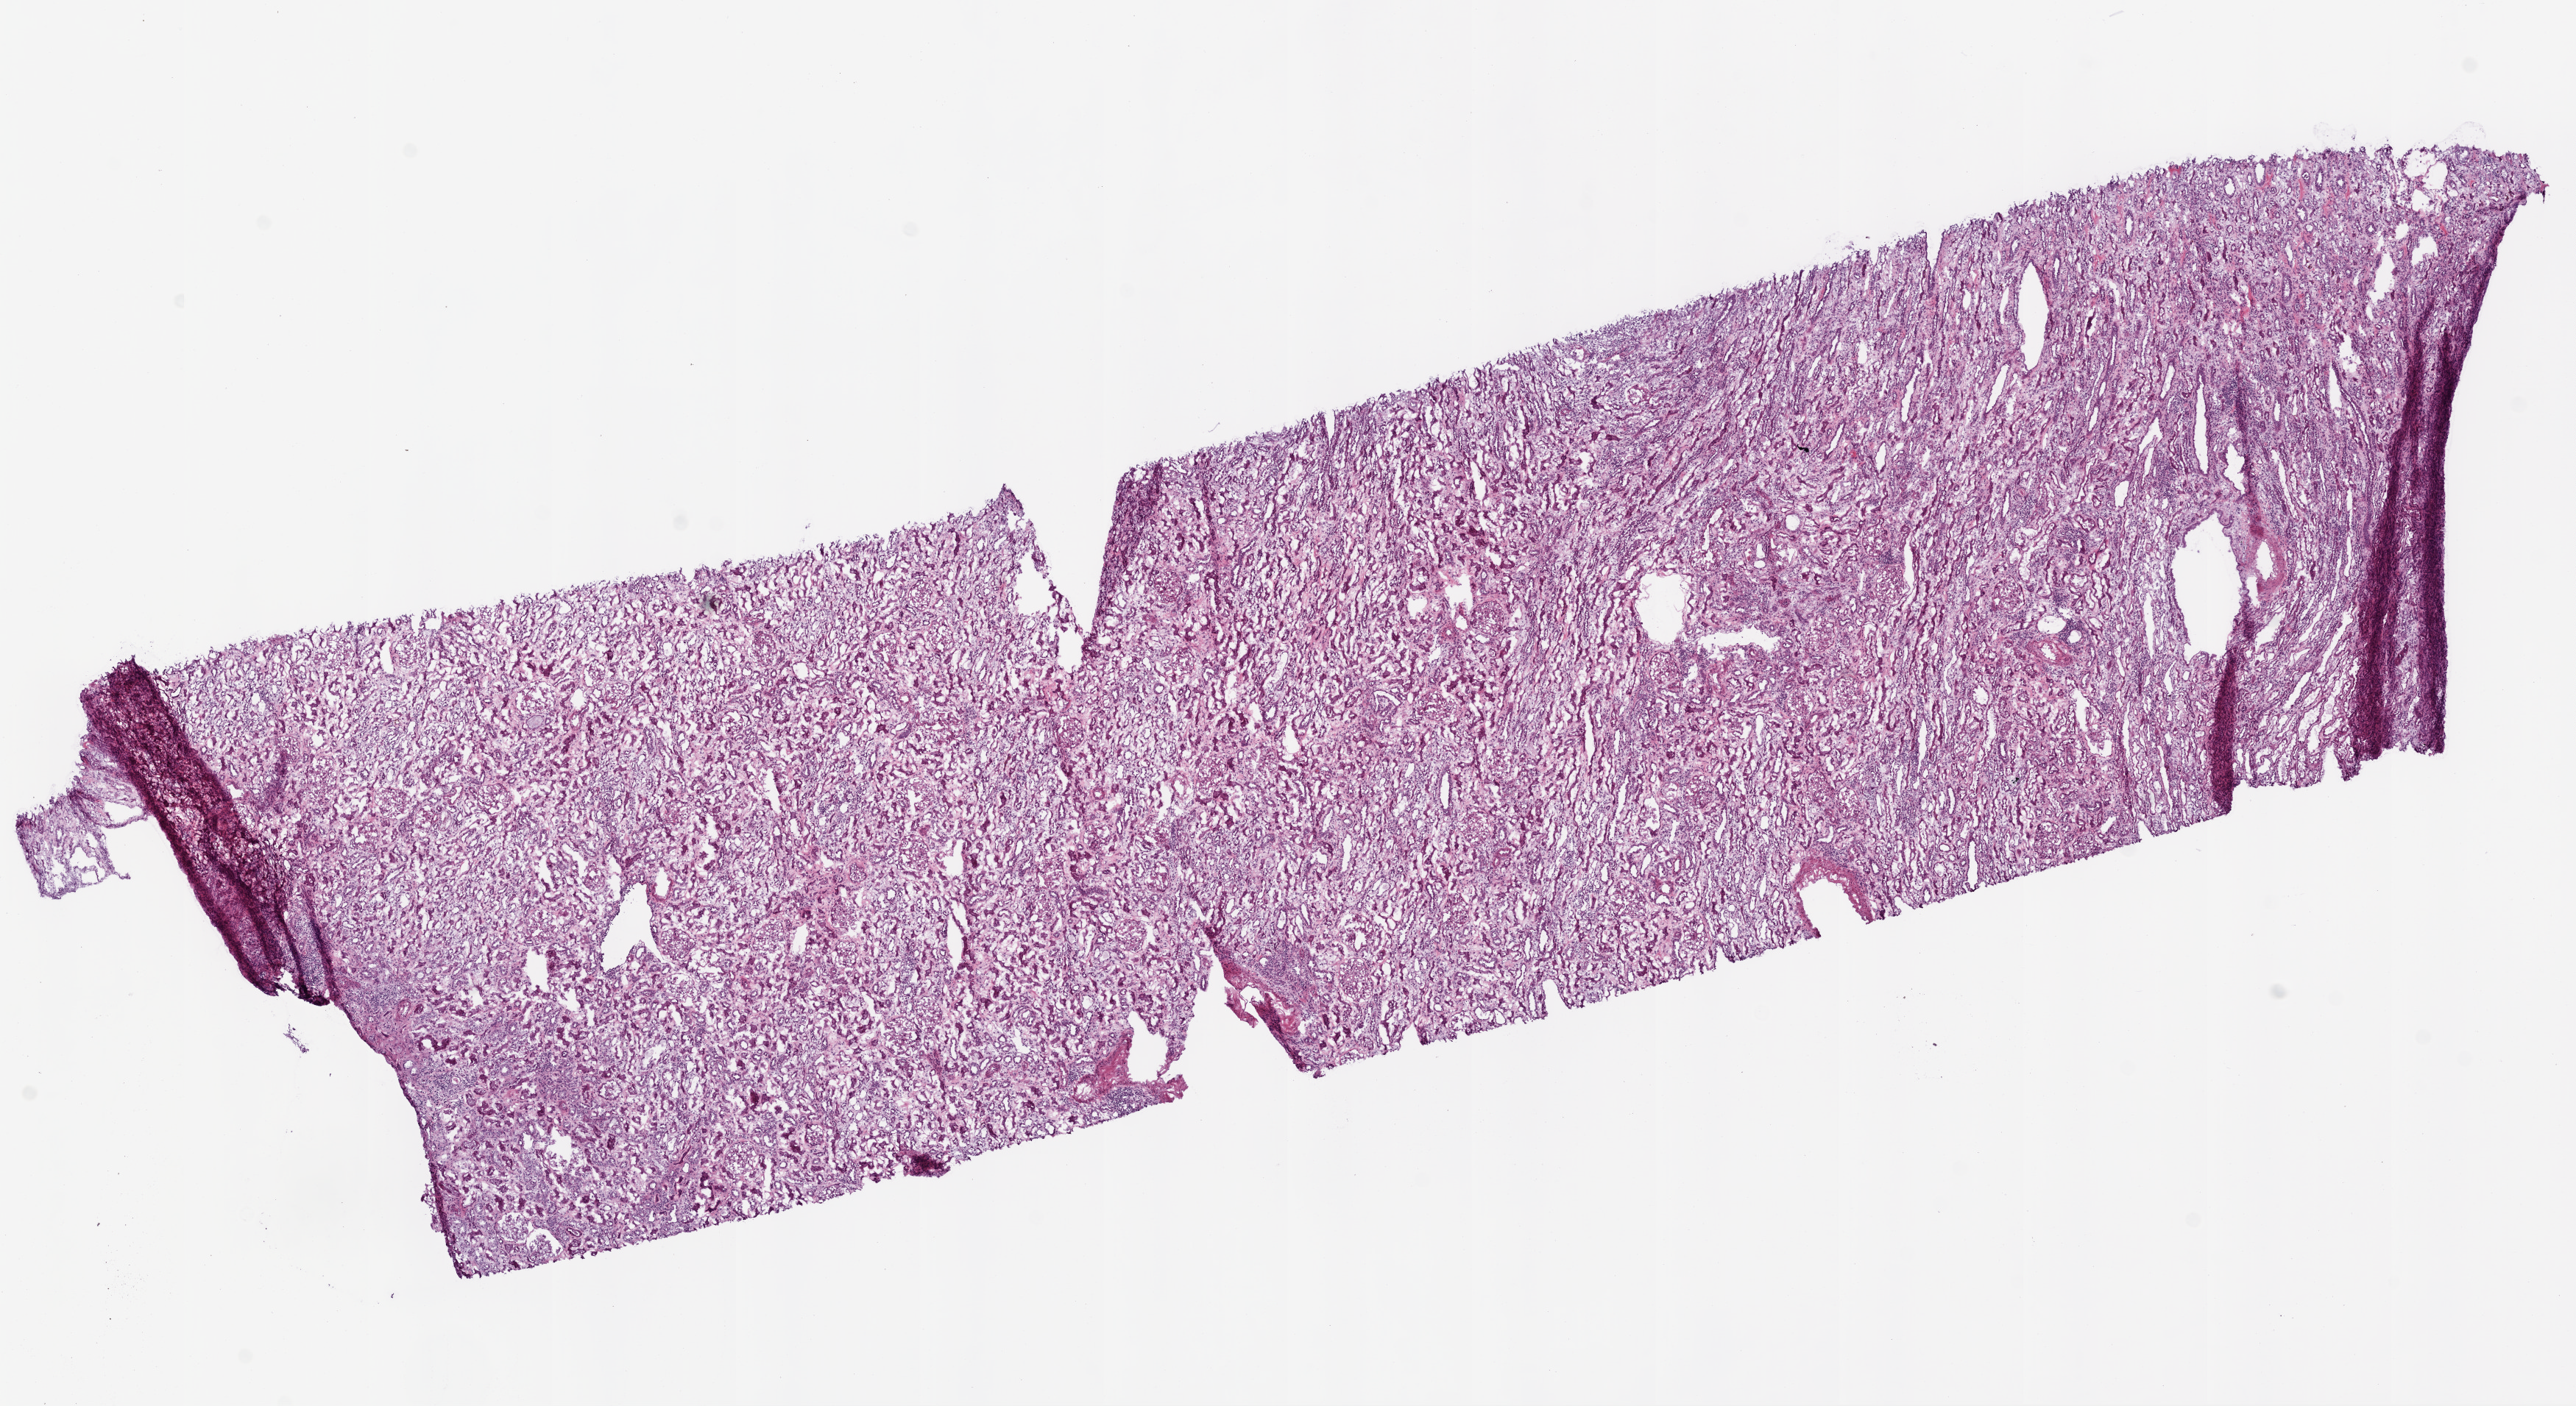
Digitized Hematoxylin and eosin (H&E) stained tissue section (whole slide), a low-resolution overview of the entire scanned area, about 14.0 x 7.7 mm, frozen section, kidney, solid tissue normal (non-tumour tissue) sample. Male, age 74 years at initial diagnosis.
This section: solid tissue normal (non-tumour) sample from the same patient. Patient diagnosis: Clear cell adenocarcinoma, NOS.